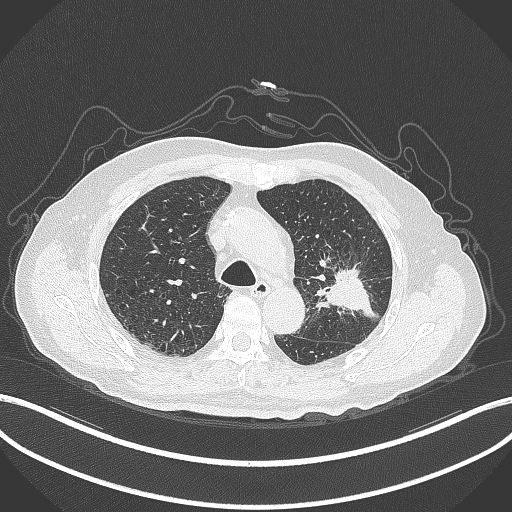
Chest CT, one axial slice; position 204 of 331 along the scan axis; 120 kVp; lung window (W 1500 / L -600 HU); 1 mm slice thickness; 512 × 512 image matrix, field of view 400 × 400 mm. Patient: male, 79 years. Case-level facts recorded for this patient, not image findings: clinical TNM (as recorded): T2a N1 M1; histopathological grade: G3.
Outlined on this slice (bounding box drawn by a radiologist):
- lung tumour (recorded histology: adenocarcinoma): bounding box [x1, y1, x2, y2] px = [315, 264, 379, 321]